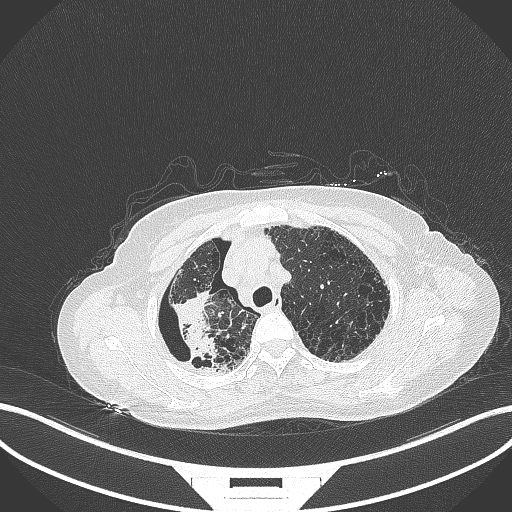
Chest CT, one axial slice; slice 288 of 408 in the series (ordered by position); 120 kVp; lung window (W 1500 / L -600 HU); 1 mm slice thickness; 512 × 512 image matrix. Patient: female, 64 years. Case-level facts recorded for this patient, not image findings: clinical TNM (as recorded): T3 N3 M0.
Outlined on this slice (rectangle marked by the reading radiologist):
- lung tumour (recorded histology: squamous cell carcinoma): bounding box <168,282,222,369> (left, top, right, bottom; pixels)